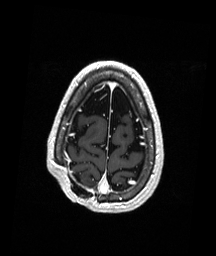
Brain MRI from a brain-tumour surgery series, one axial slice. Position 46 of 192 along the scan axis. T1-weighted post-contrast. 1 mm slice thickness. 216 × 256 image matrix. From the clinical record (not read from this slice): histopathology: Astrocytoma; WHO grade: 3; IDH mutation: yes; tumour location: Right Parietal.
Structures marked on this image (manually delineated by an expert):
- previous resection cavity: bounding box (x1, y1, x2, y2) in pixels: (73, 175, 80, 183)